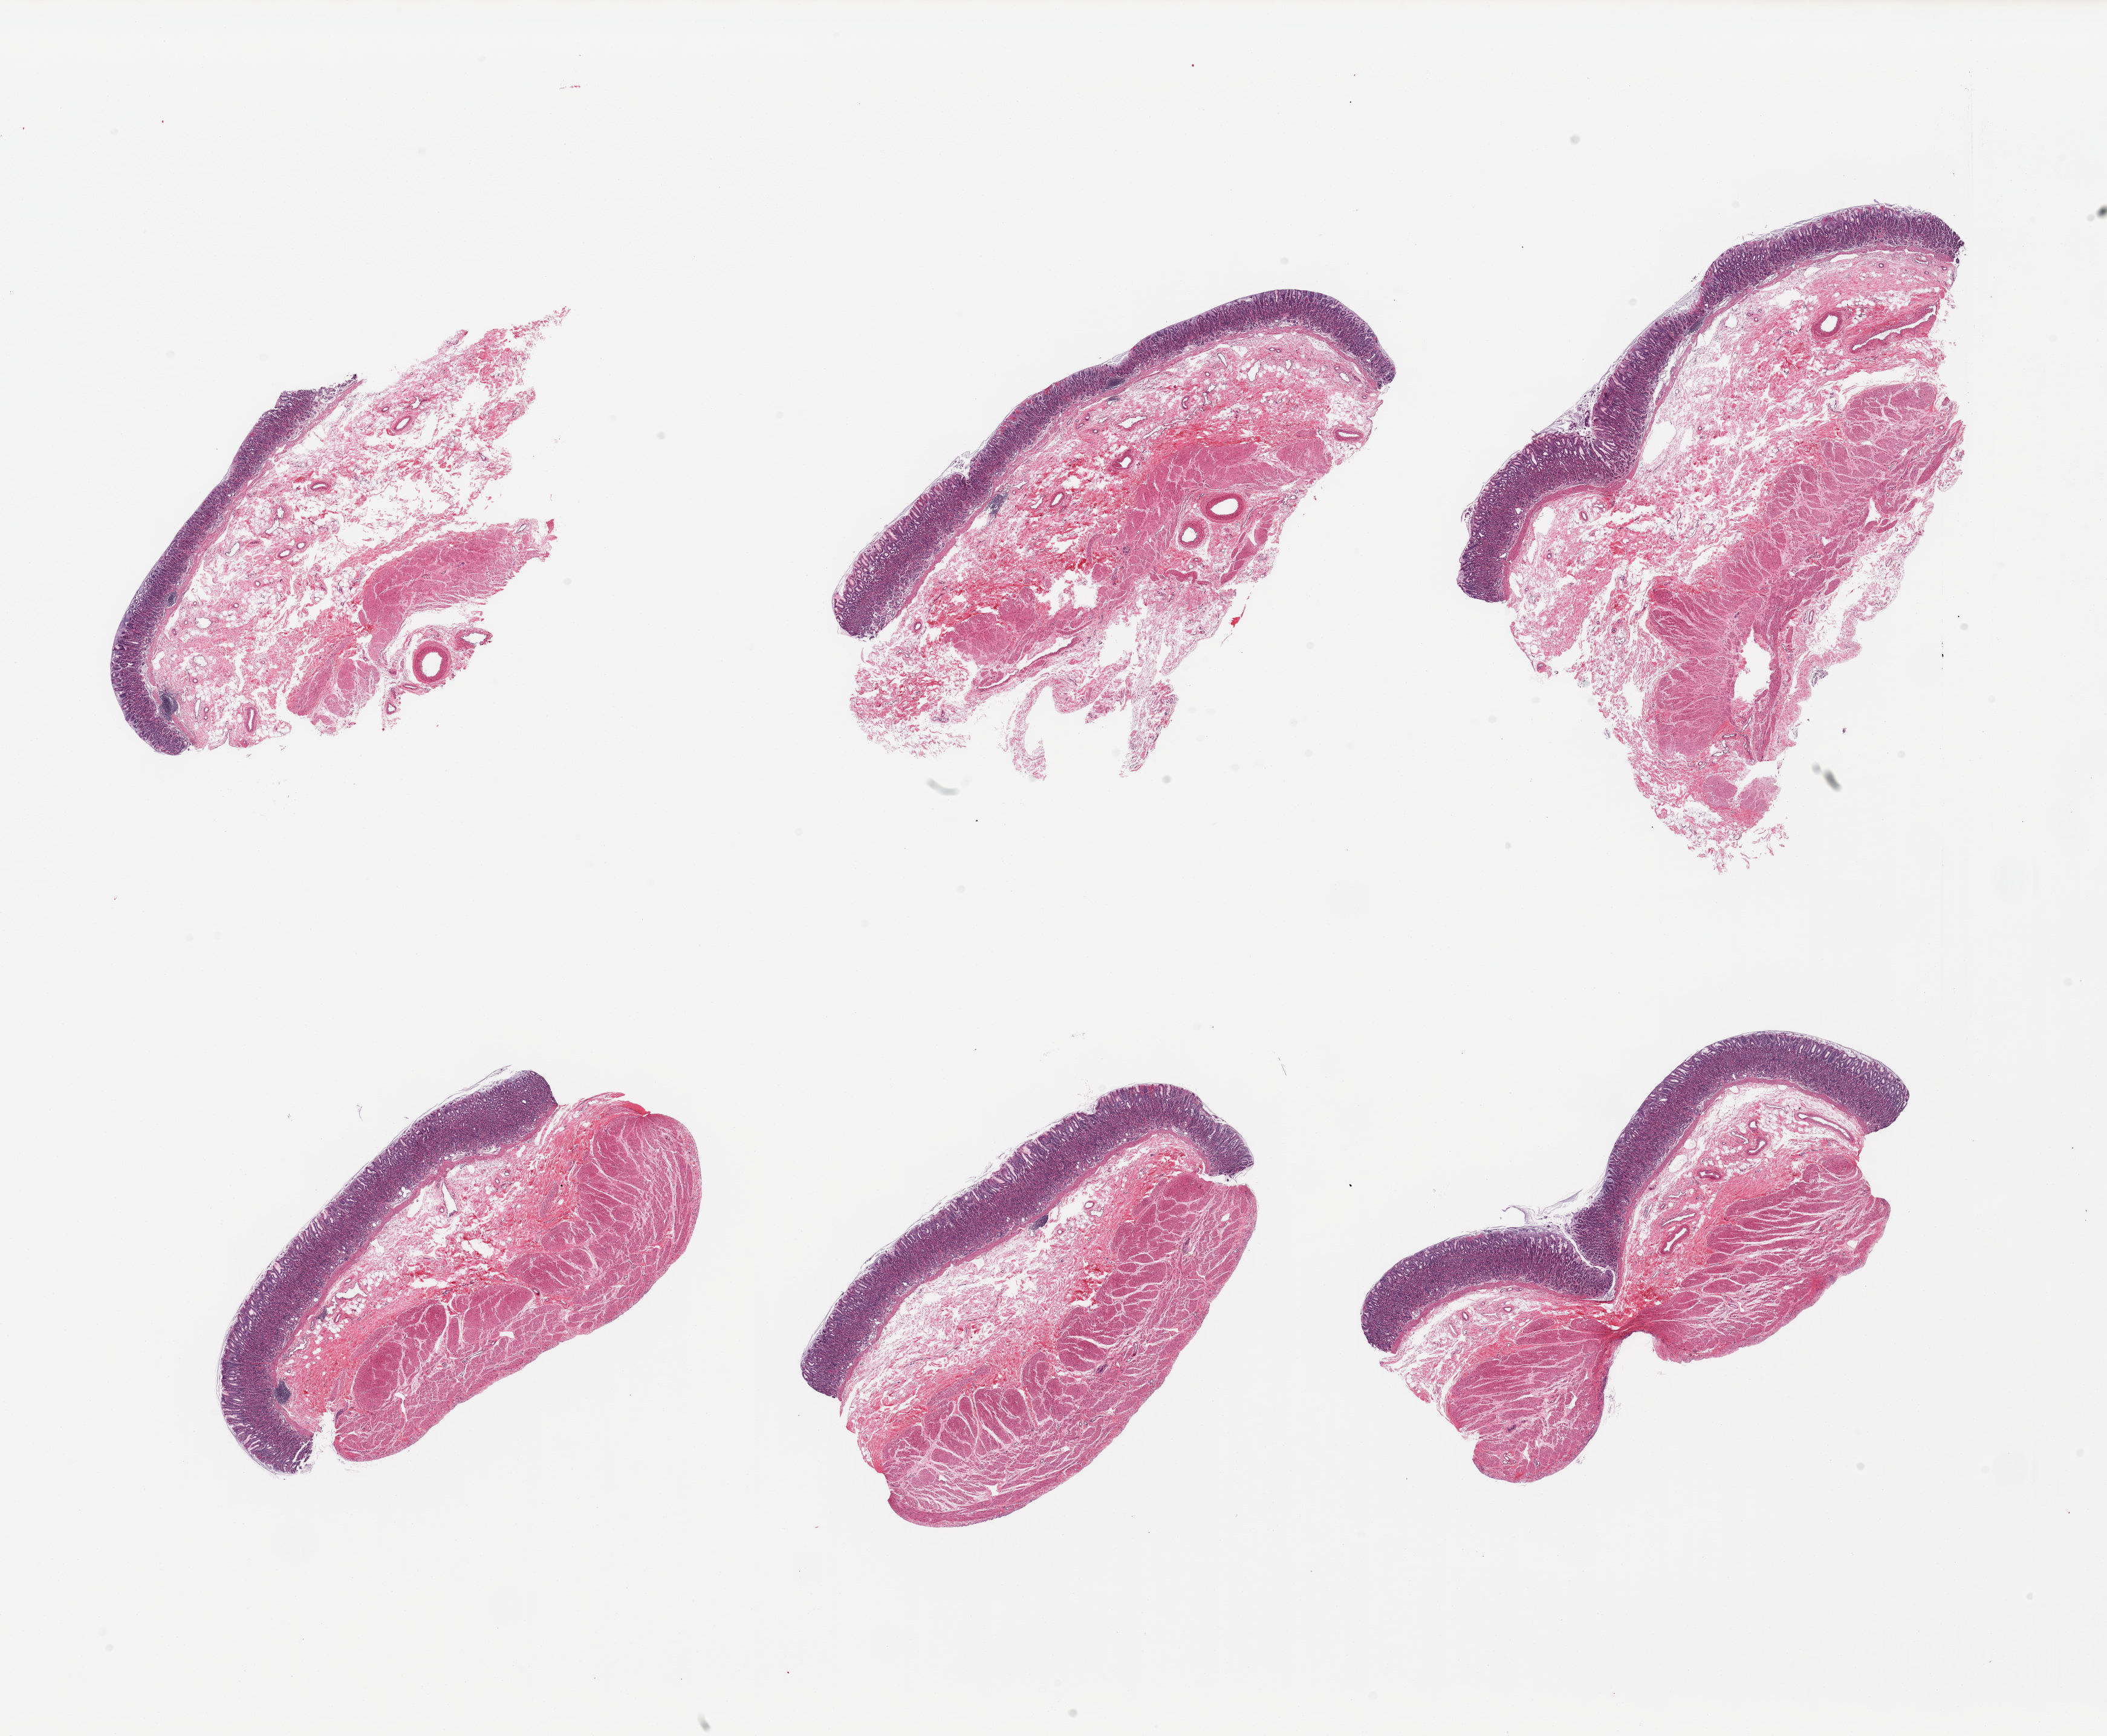
Whole-slide image, hematoxylin and eosin (H&E) stain, brightfield — shown as a low-resolution overview of the whole scanned area (about 27.6 x 22.7 mm). PAXgene-fixed, paraffin-embedded tissue. Section of stomach (target tissue). Tissue donor sample.
Review note (as recorded): 6 pieces; full thickness; well dissected.